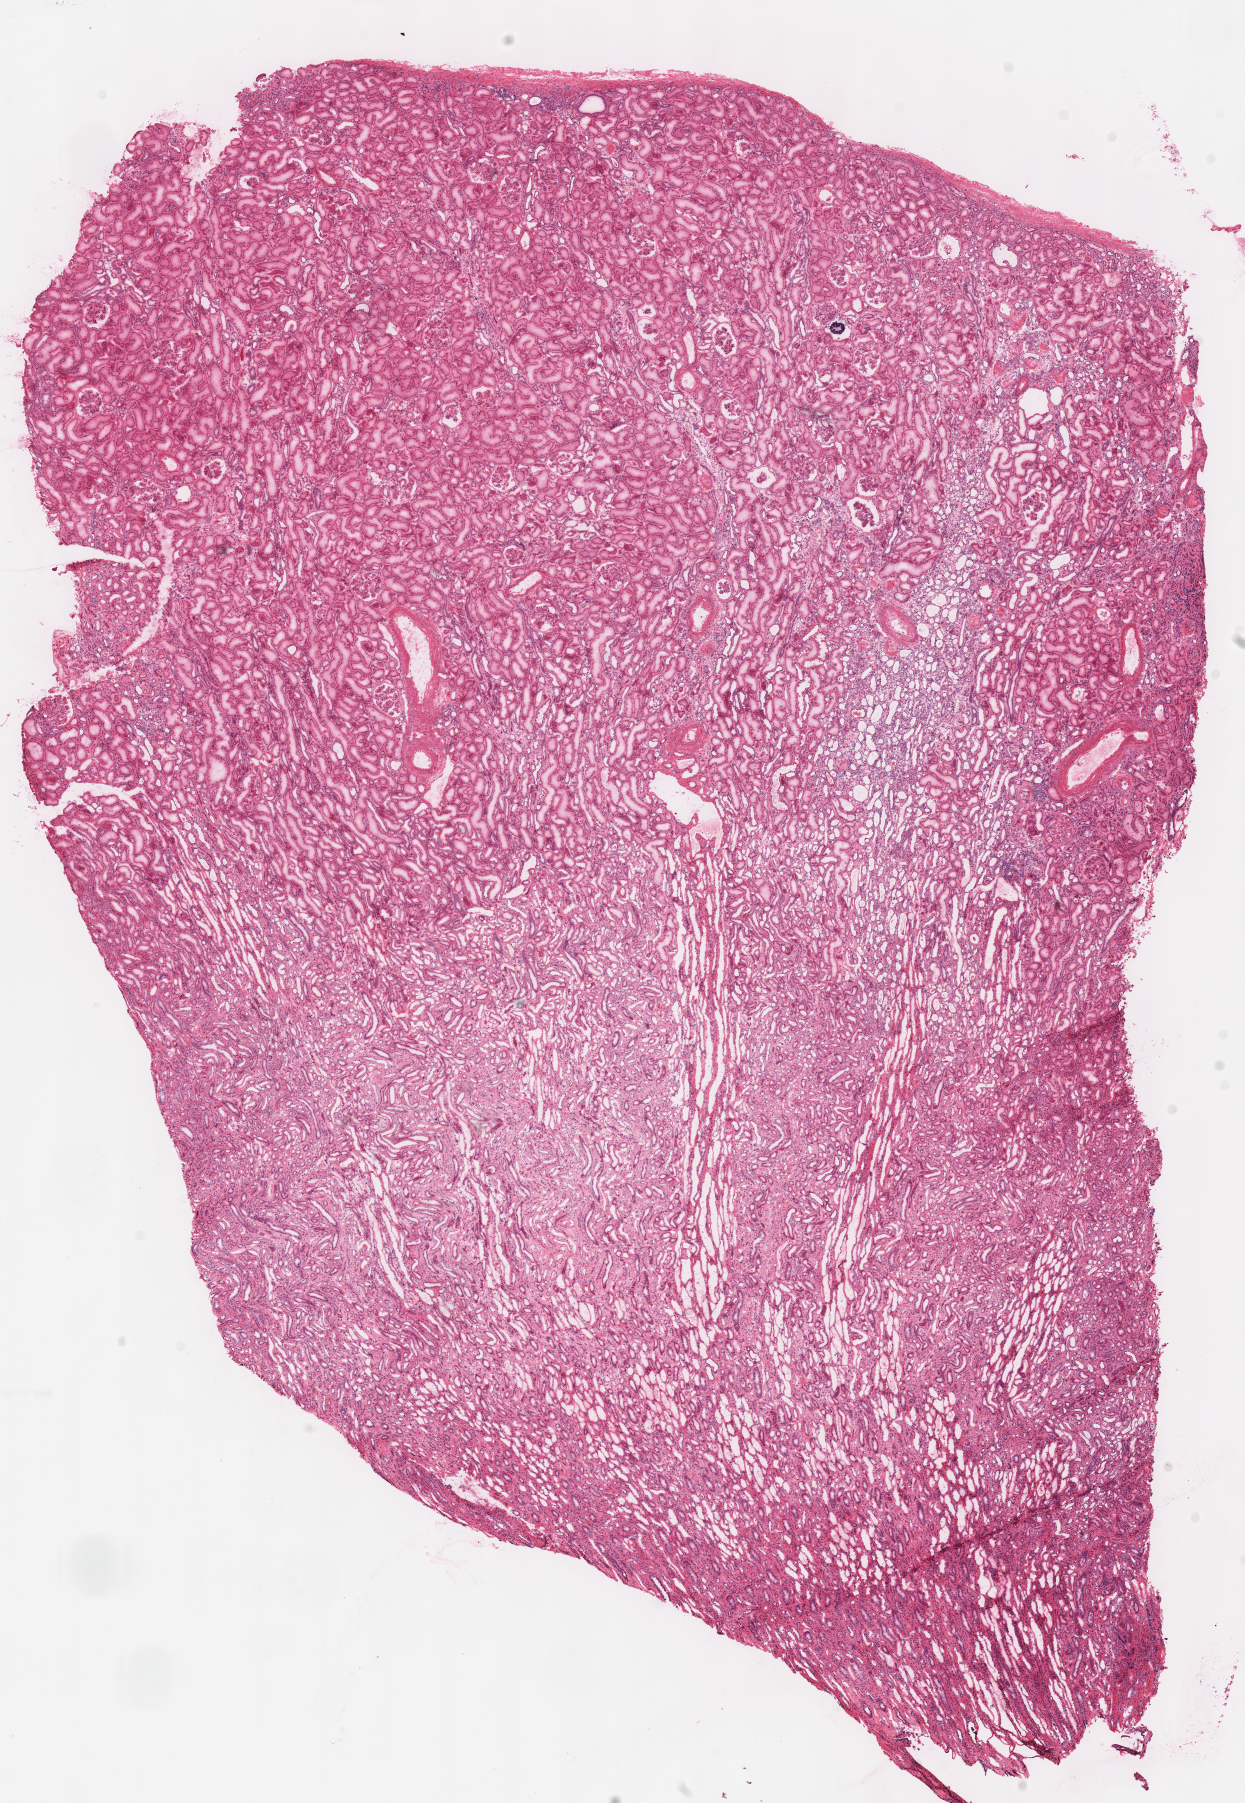
Whole-slide histology image, H&E-stained, shown as a low-resolution overview of the whole scanned area (about 9.8 x 14.2 mm, slide scanned at 40x); frozen section; kidney, solid tissue normal (non-tumour tissue) sample. Female patient; age at initial diagnosis 67 years. Infiltration values recorded for this section: lymphocyte infiltration 3%, monocyte infiltration 0%, neutrophil infiltration 0%.
• this section: solid tissue normal (non-tumour) sample from the same patient
• patient diagnosis: Renal cell carcinoma, chromophobe type